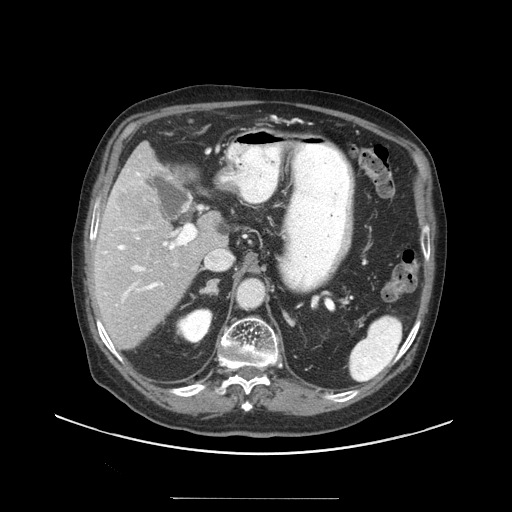
Contrast-enhanced abdominal CT (liver protocol), one axial slice; position 61 of 97 along the scan axis; reconstruction kernel STANDARD; soft-tissue window (W 400 / L 40 HU); 2.5 mm slice thickness; 512 × 512 image matrix, field of view 450 × 450 mm. From the clinical record (not read from this slice): diagnosis: hepatocellular carcinoma (patient treated with transarterial chemoembolisation; whether this scan precedes or follows treatment is not stated here); TNM stage (as recorded): Stage-IIIC.
Annotated regions visible in this slice (semi-automatic segmentation, software-assisted and operator-edited):
- liver parenchyma outside the tumour (the mass and vessels are separate outlines, so this box may not span the whole liver): bounding box (x1, y1, x2, y2) in pixels: (92, 142, 226, 348)
- mass: (116, 186, 161, 229)
- liver vessels: (102, 172, 186, 302)